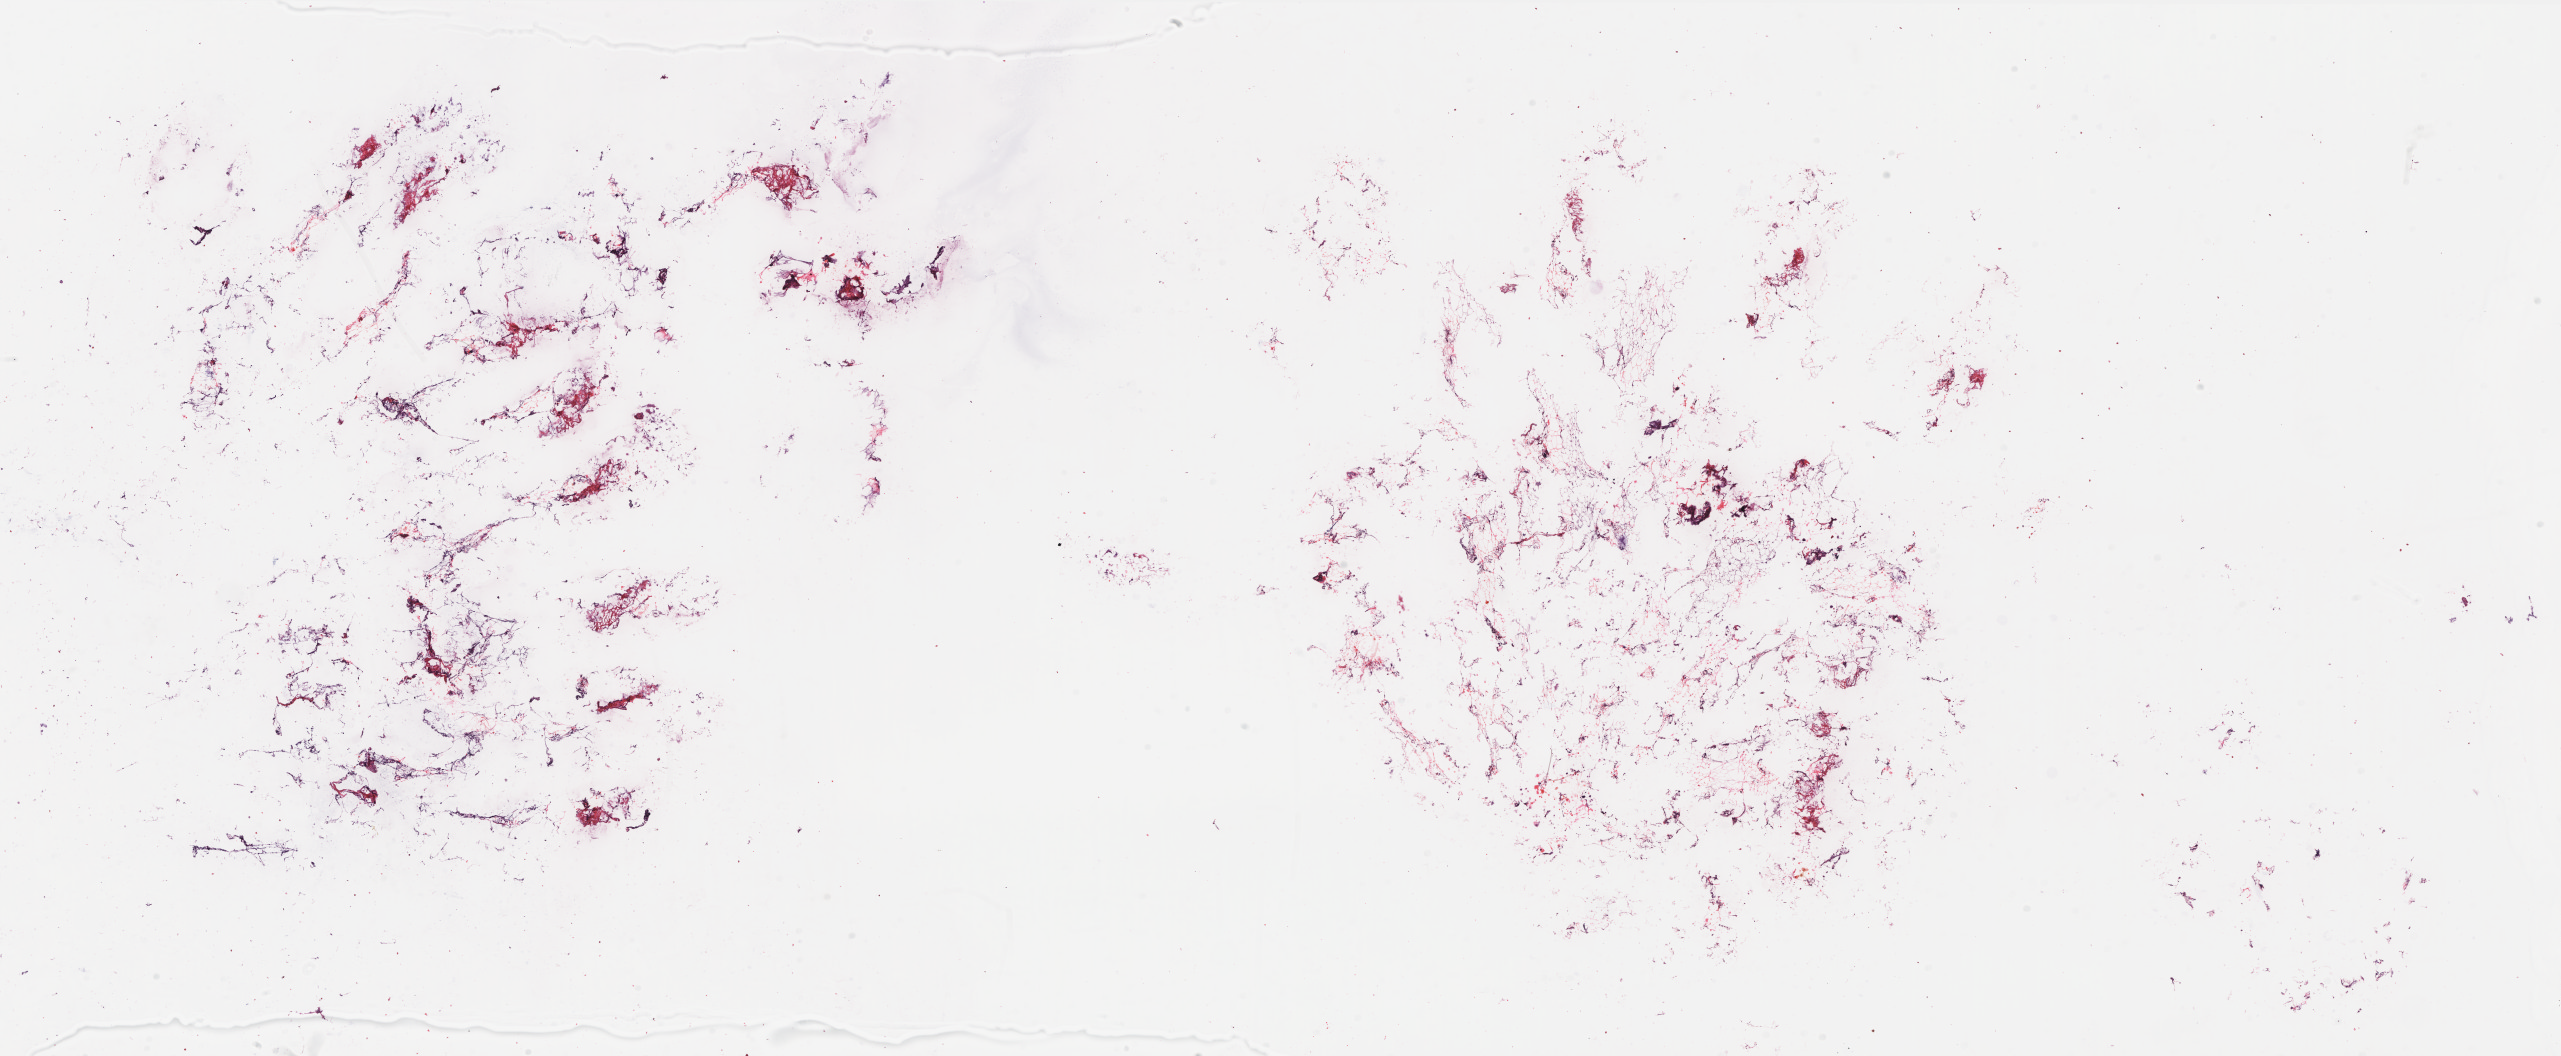
Digitized H&E-stained tissue section (whole slide), low-resolution overview of the scanned area, about 40.9 x 16.9 mm (acquisition: 20x scan). Frozen section from the top of the tissue portion. Breast, solid tissue normal (non-tumour tissue) sample. Female patient; age at initial diagnosis 63 years.
This section: solid tissue normal (non-tumour) sample from the same patient. Patient diagnosis: Infiltrating duct carcinoma, NOS.